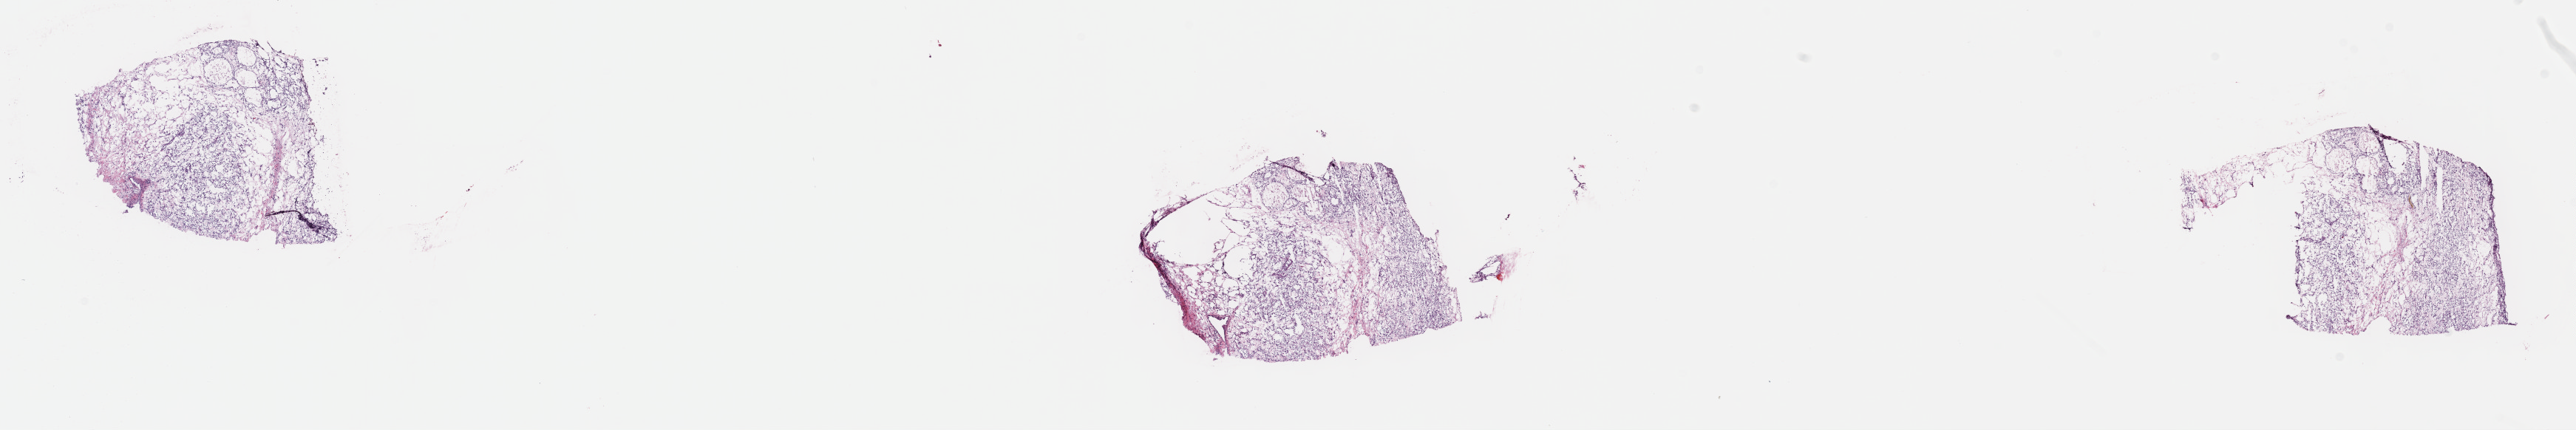
H&E-stained whole-slide image — a low-resolution overview of the entire scanned area, about 28.2 x 4.7 mm, frozen section from the top of the tissue portion, sample: primary tumour, kidney. Female patient; age at initial diagnosis 54 years. Histologic grade: G3 (poorly differentiated). Composition of this section per pathologist review: tumour cells 60%, tumour nuclei 90%, normal cells 0%, stromal cells 25%, necrosis 15%. Inflammatory infiltration, as recorded: lymphocyte infiltration 3%, monocyte infiltration 2%, neutrophil infiltration 0%.
AJCC pathologic stage: I (7th edition). Laterality: left. TNM: T1a NX. Diagnosis: Clear cell adenocarcinoma, NOS.